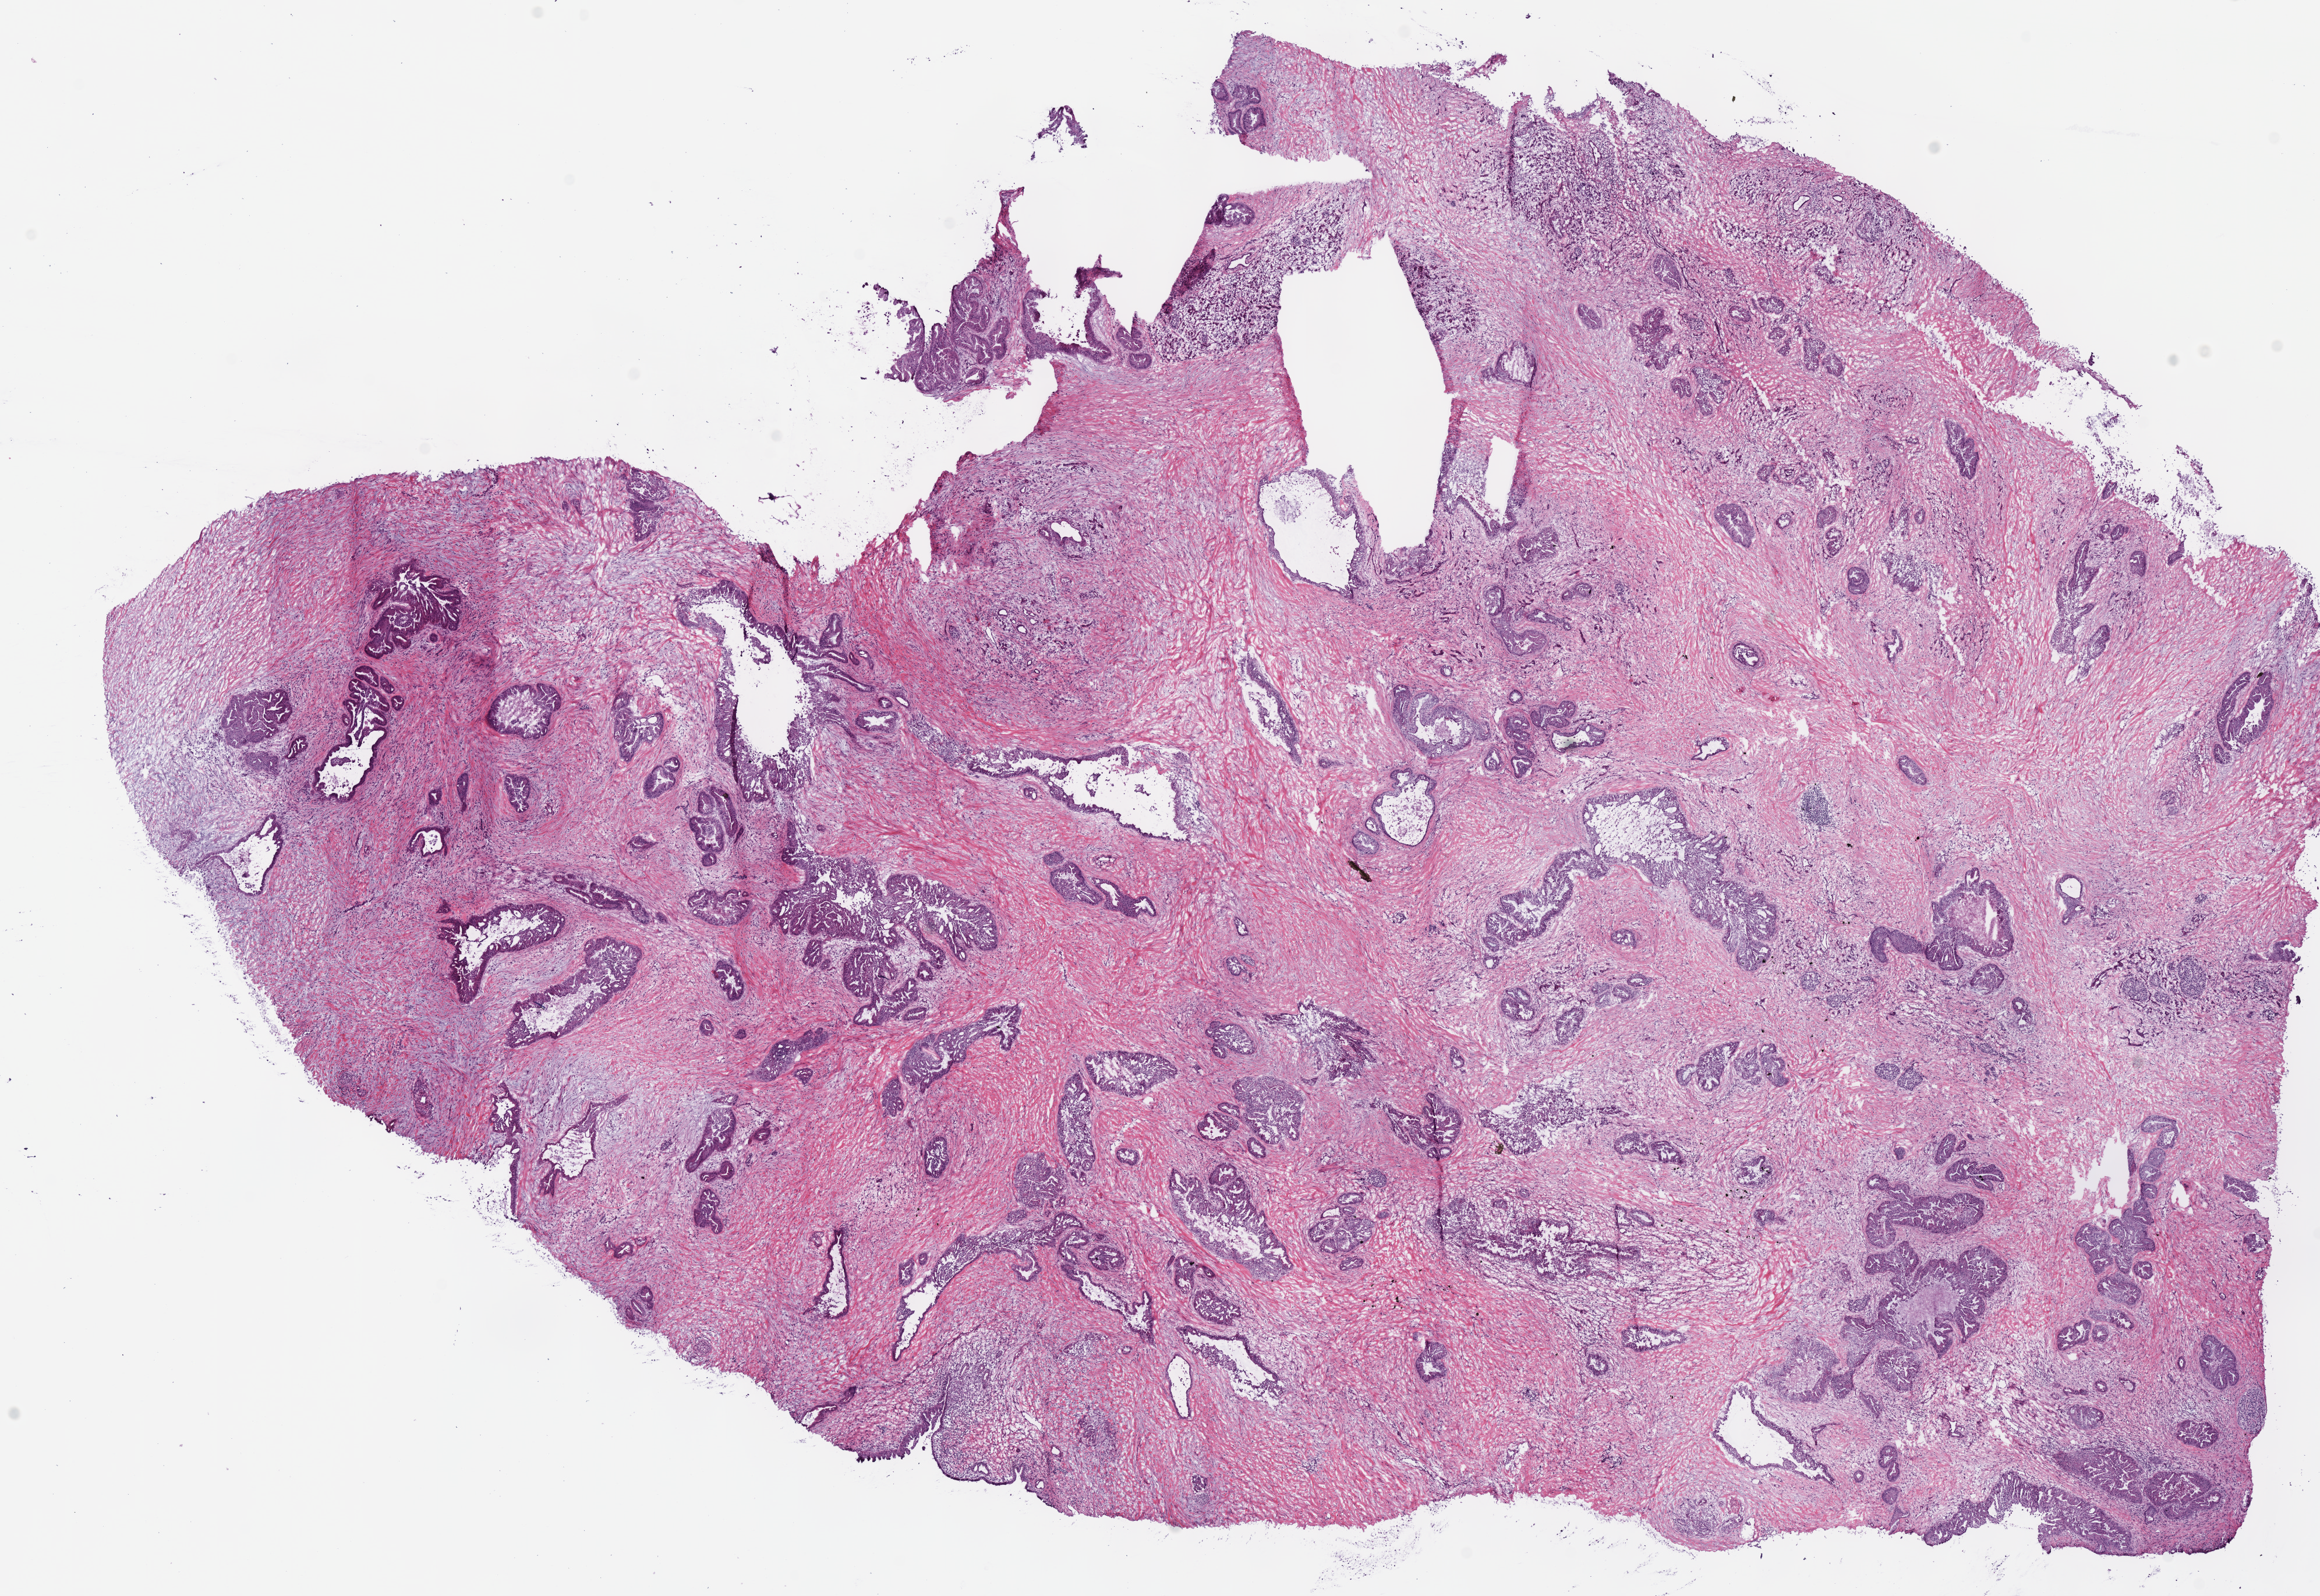
Whole-slide histology image, H&E — shown as a low-resolution overview of the whole scanned area (about 15.7 x 10.8 mm, acquisition: 40x scan). Frozen section from the bottom of the tissue portion. Primary tumour sample from the pancreas. Patient: female, age at initial diagnosis 49 years. Histologic grade: G2 (moderately differentiated). Pathologist review of this section (percent, as recorded): tumour cells 97%, tumour nuclei 80%, normal cells 0%, stromal cells 0%, necrosis 3%. Inflammatory infiltration, as recorded: lymphocyte infiltration 2%, monocyte infiltration 0%, neutrophil infiltration 0%.
* pathologic diagnosis: Infiltrating duct carcinoma, NOS
* AJCC pathologic stage: IIB (7th edition)
* lymph nodes positive (case pathology): 1 of 20 examined